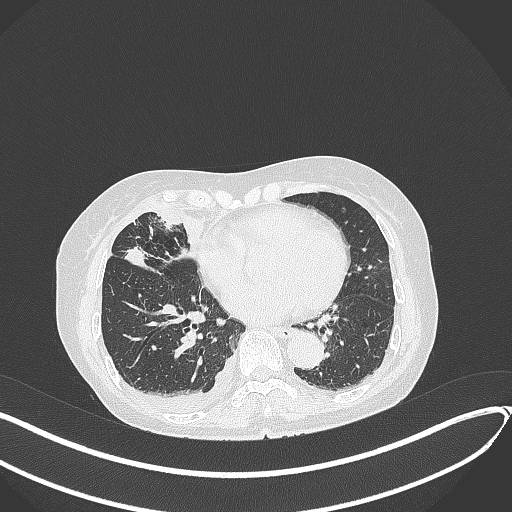
Chest CT, one axial slice; slice 155 of 418 in the series (ordered by position); 120 kVp; lung window (W 1500 / L -600 HU); 1 mm slice thickness; 512 × 512 image matrix. Female patient, age 75 years. Case-level facts recorded for this patient, not image findings: clinical TNM (as recorded): T2a N3 M0.
Structures marked on this image (rectangle marked by the reading radiologist):
- lung tumour (recorded histology: adenocarcinoma): bounding box [x1, y1, x2, y2] px = [123, 244, 158, 270]